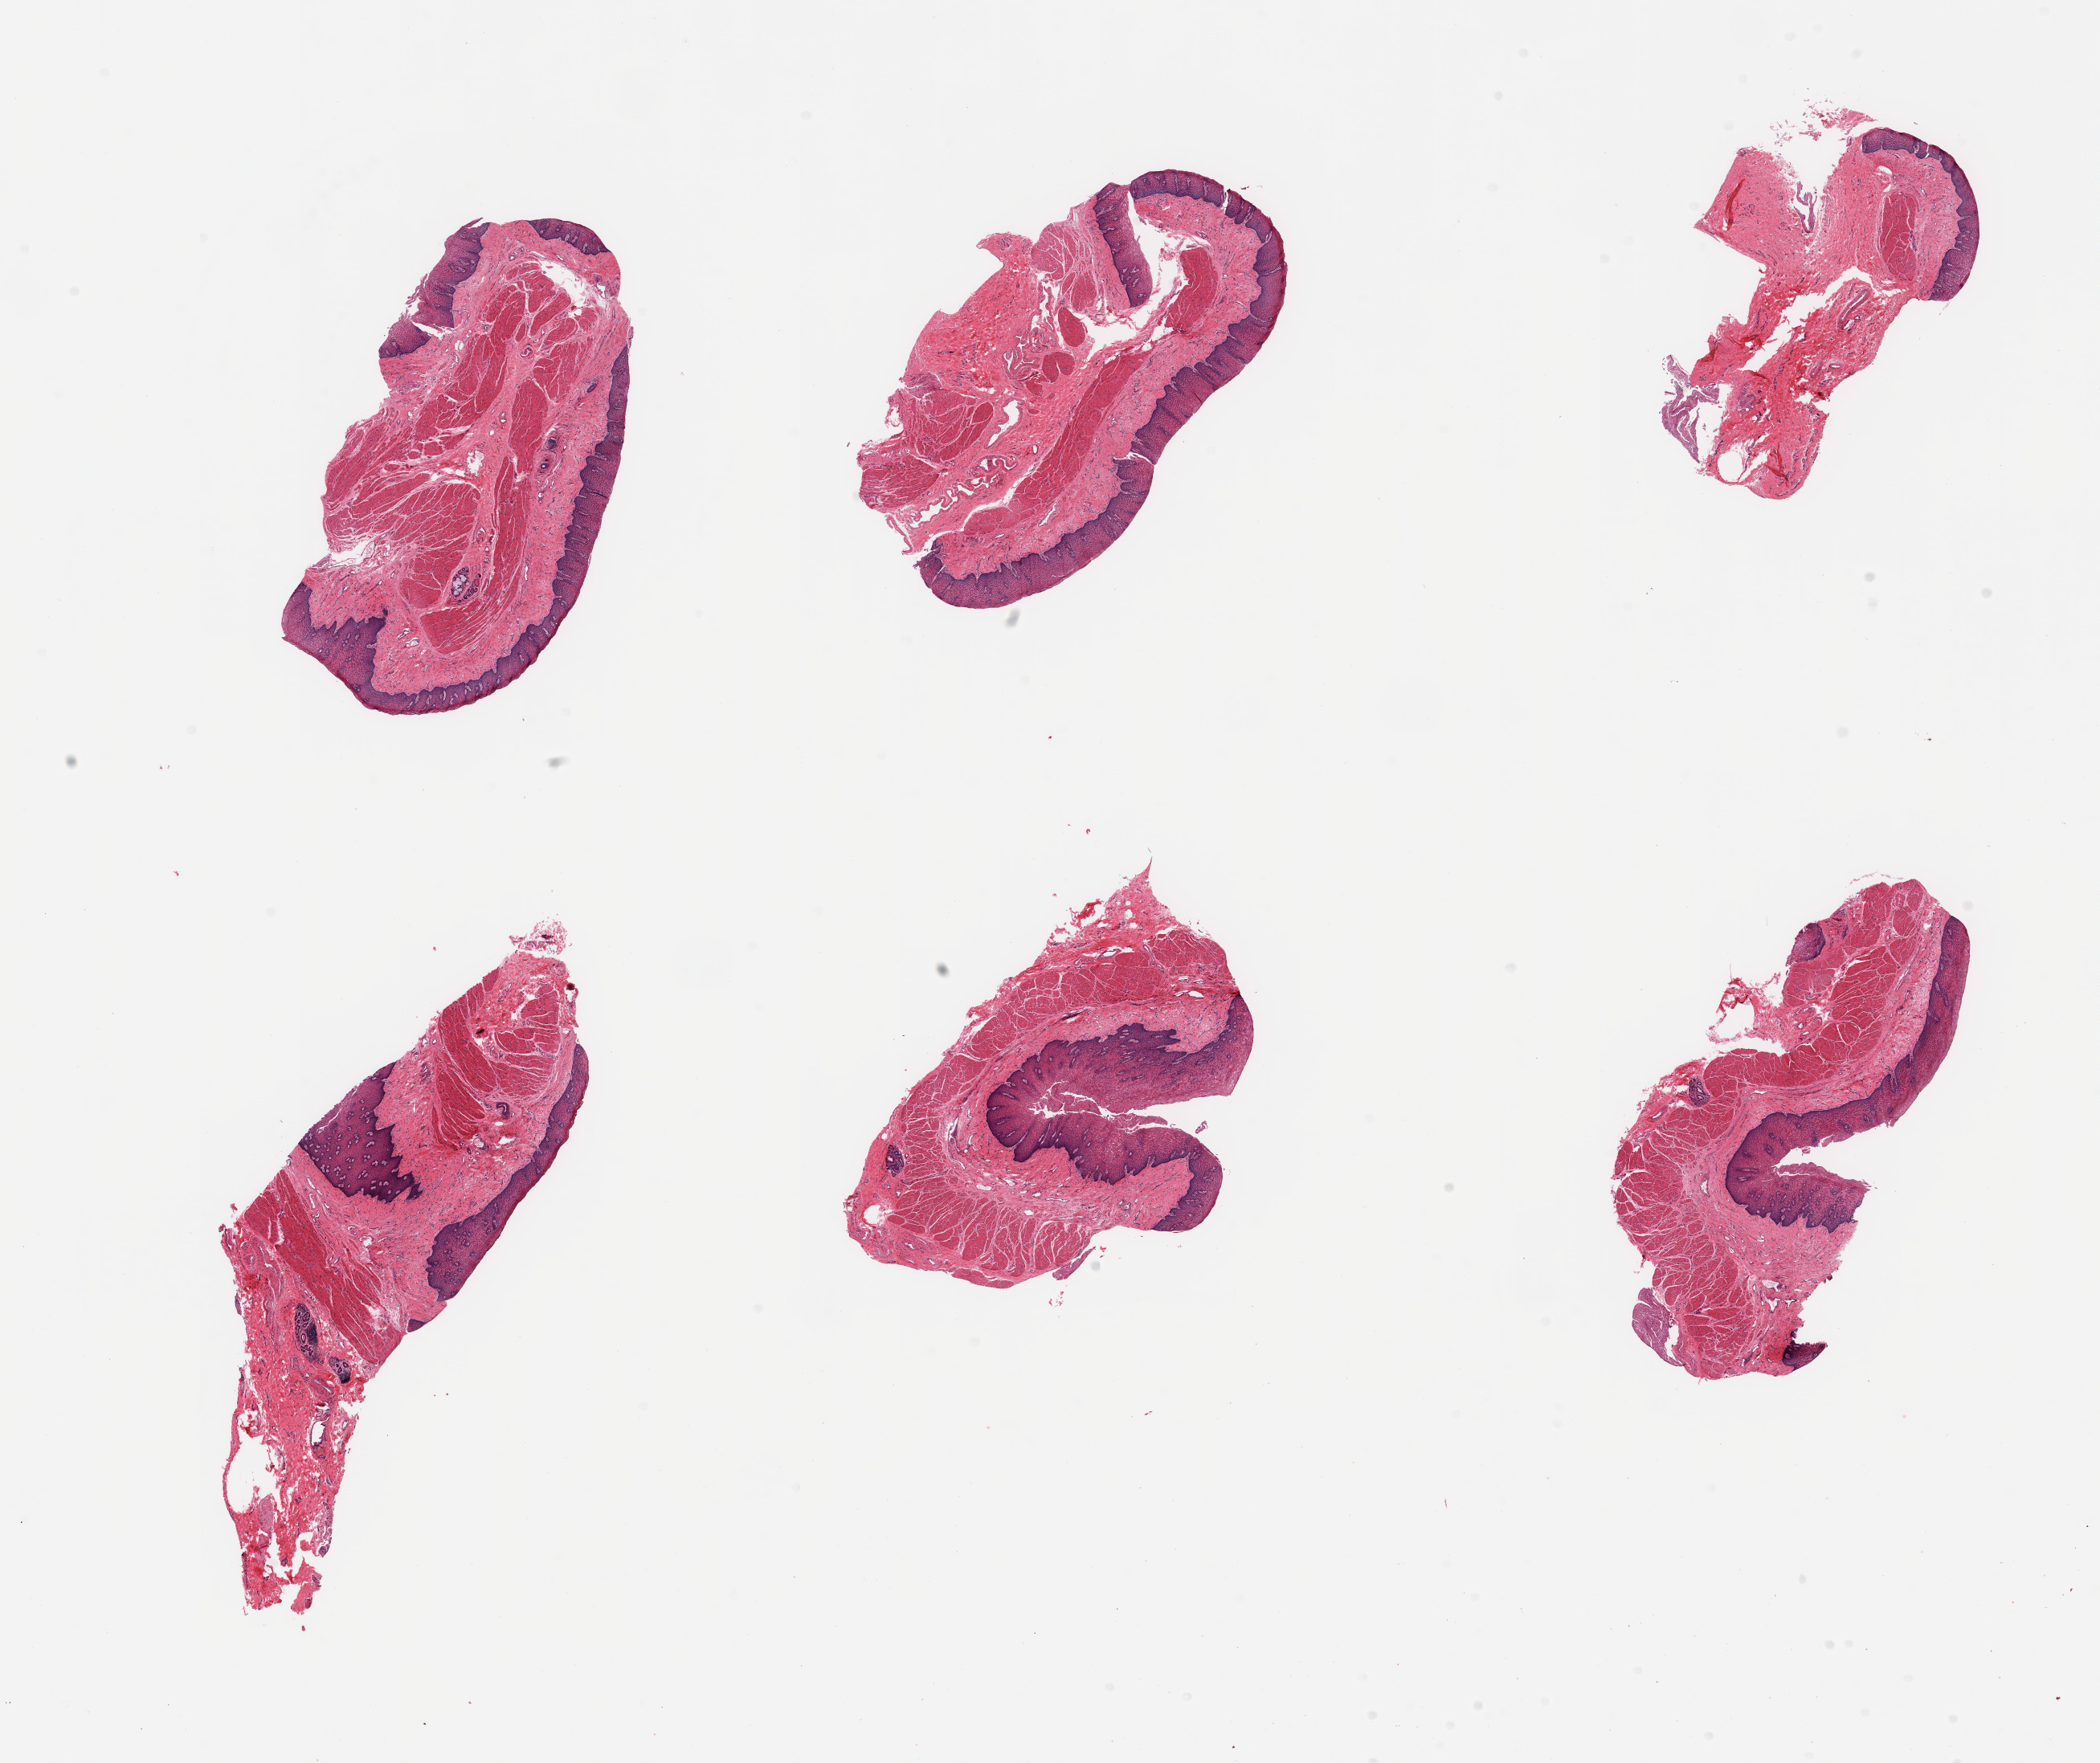
Haematoxylin and eosin whole-slide image, brightfield — low-resolution overview of the scanned area, about 20.7 x 17.4 mm (from a 20x scan); PAXgene-fixed paraffin-embedded (PFPE) section; sampled site (target tissue): esophageal mucous membrane; tissue donor sample.
* review note (as recorded): 6 pieces, mucosa up to ~0.3mm, 15-20% thickness